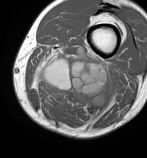
MRI of an extremity soft-tissue mass, one axial slice; slice 27 of 86 in the series (ordered by position); MR volume resampled by the dataset authors to the PET/CT grid (not the native acquisition matrix); 3.27 mm slice thickness; 147 × 158 image matrix, field of view 144 × 154 mm. Male patient. Case-level facts recorded for this patient, not image findings: histological type: undifferentiated pleomorphic liposarcoma; grade: high; site of the primary tumour: left thigh.
Outlined on this slice (expert contour drawn on MRI and transferred to this co-registered scan by the dataset authors):
- gross tumour volume including surrounding oedema: box from (x=30, y=44) to (x=118, y=125) px
- gross tumour volume (mass): (x=41, y=60)–(x=106, y=107)